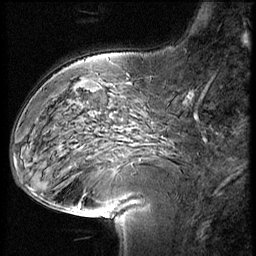
Breast MRI (dynamic contrast-enhanced), one sagittal slice. Slice 18 of 58 in the series (ordered by position). 3 images stored at this slice position (order not interpretable as contrast timing). 1.5 T. TE 4.2 ms, TR 9 ms. 2.5 mm slice thickness. 256 × 256 image matrix, field of view 180 × 180 mm. Patient: female, 57 years. From the clinical record (not read from this slice): setting: breast cancer imaged before/during neoadjuvant chemotherapy; receptor status: HER2-positive.
Outlined on this slice (semi-automatic segmentation, software-assisted and operator-edited):
- analysis volume of interest (the breast-tissue region the enhancement analysis was run in; not a lesion): bounding box [x1, y1, x2, y2] px = [79, 110, 174, 205]
- tumour enhancement mask (voxels above the 140 % enhancement threshold inside the analysis volume of interest): [133, 202, 137, 204]